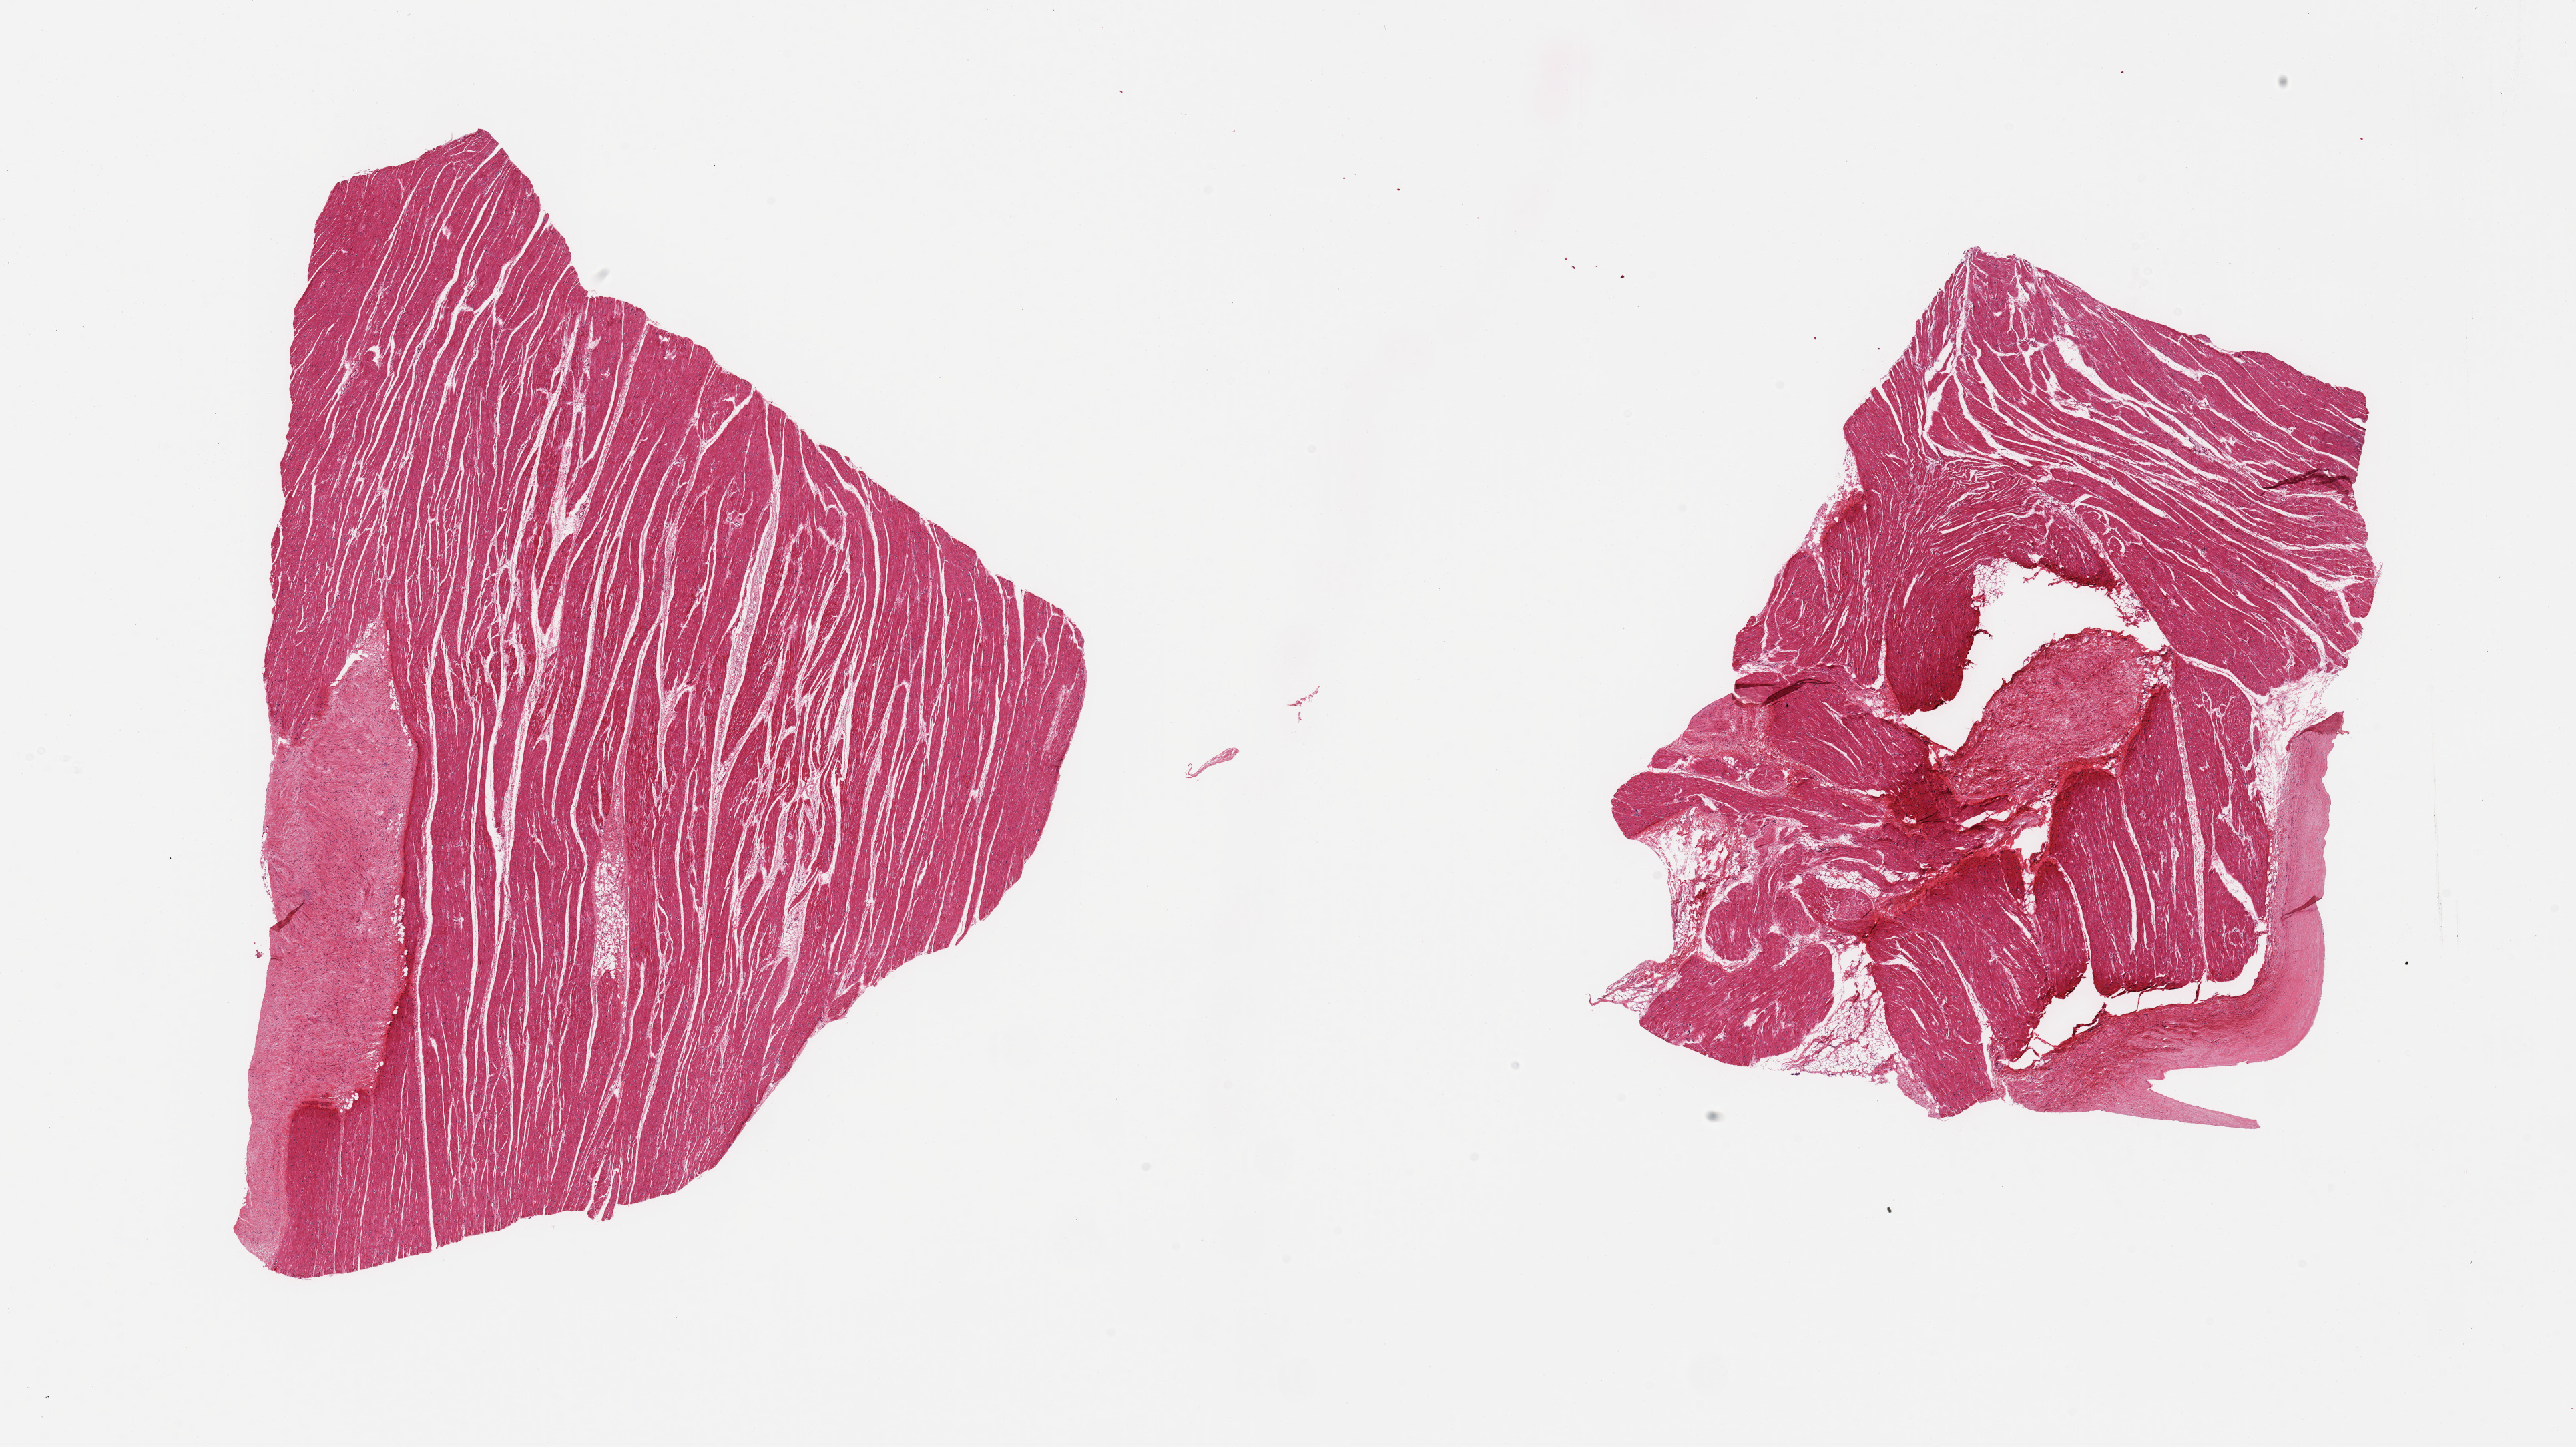
Hematoxylin and eosin (H&E) whole-slide image — a low-resolution overview of the entire scanned area, about 30.5 x 17.1 mm; PAXgene-fixed paraffin-embedded (PFPE) section; section of auricular appendage (target tissue); tissue donor sample. Male donor.
• pathologist's review note for this sample: 2 pieces, mild intersitial chronic inflammation